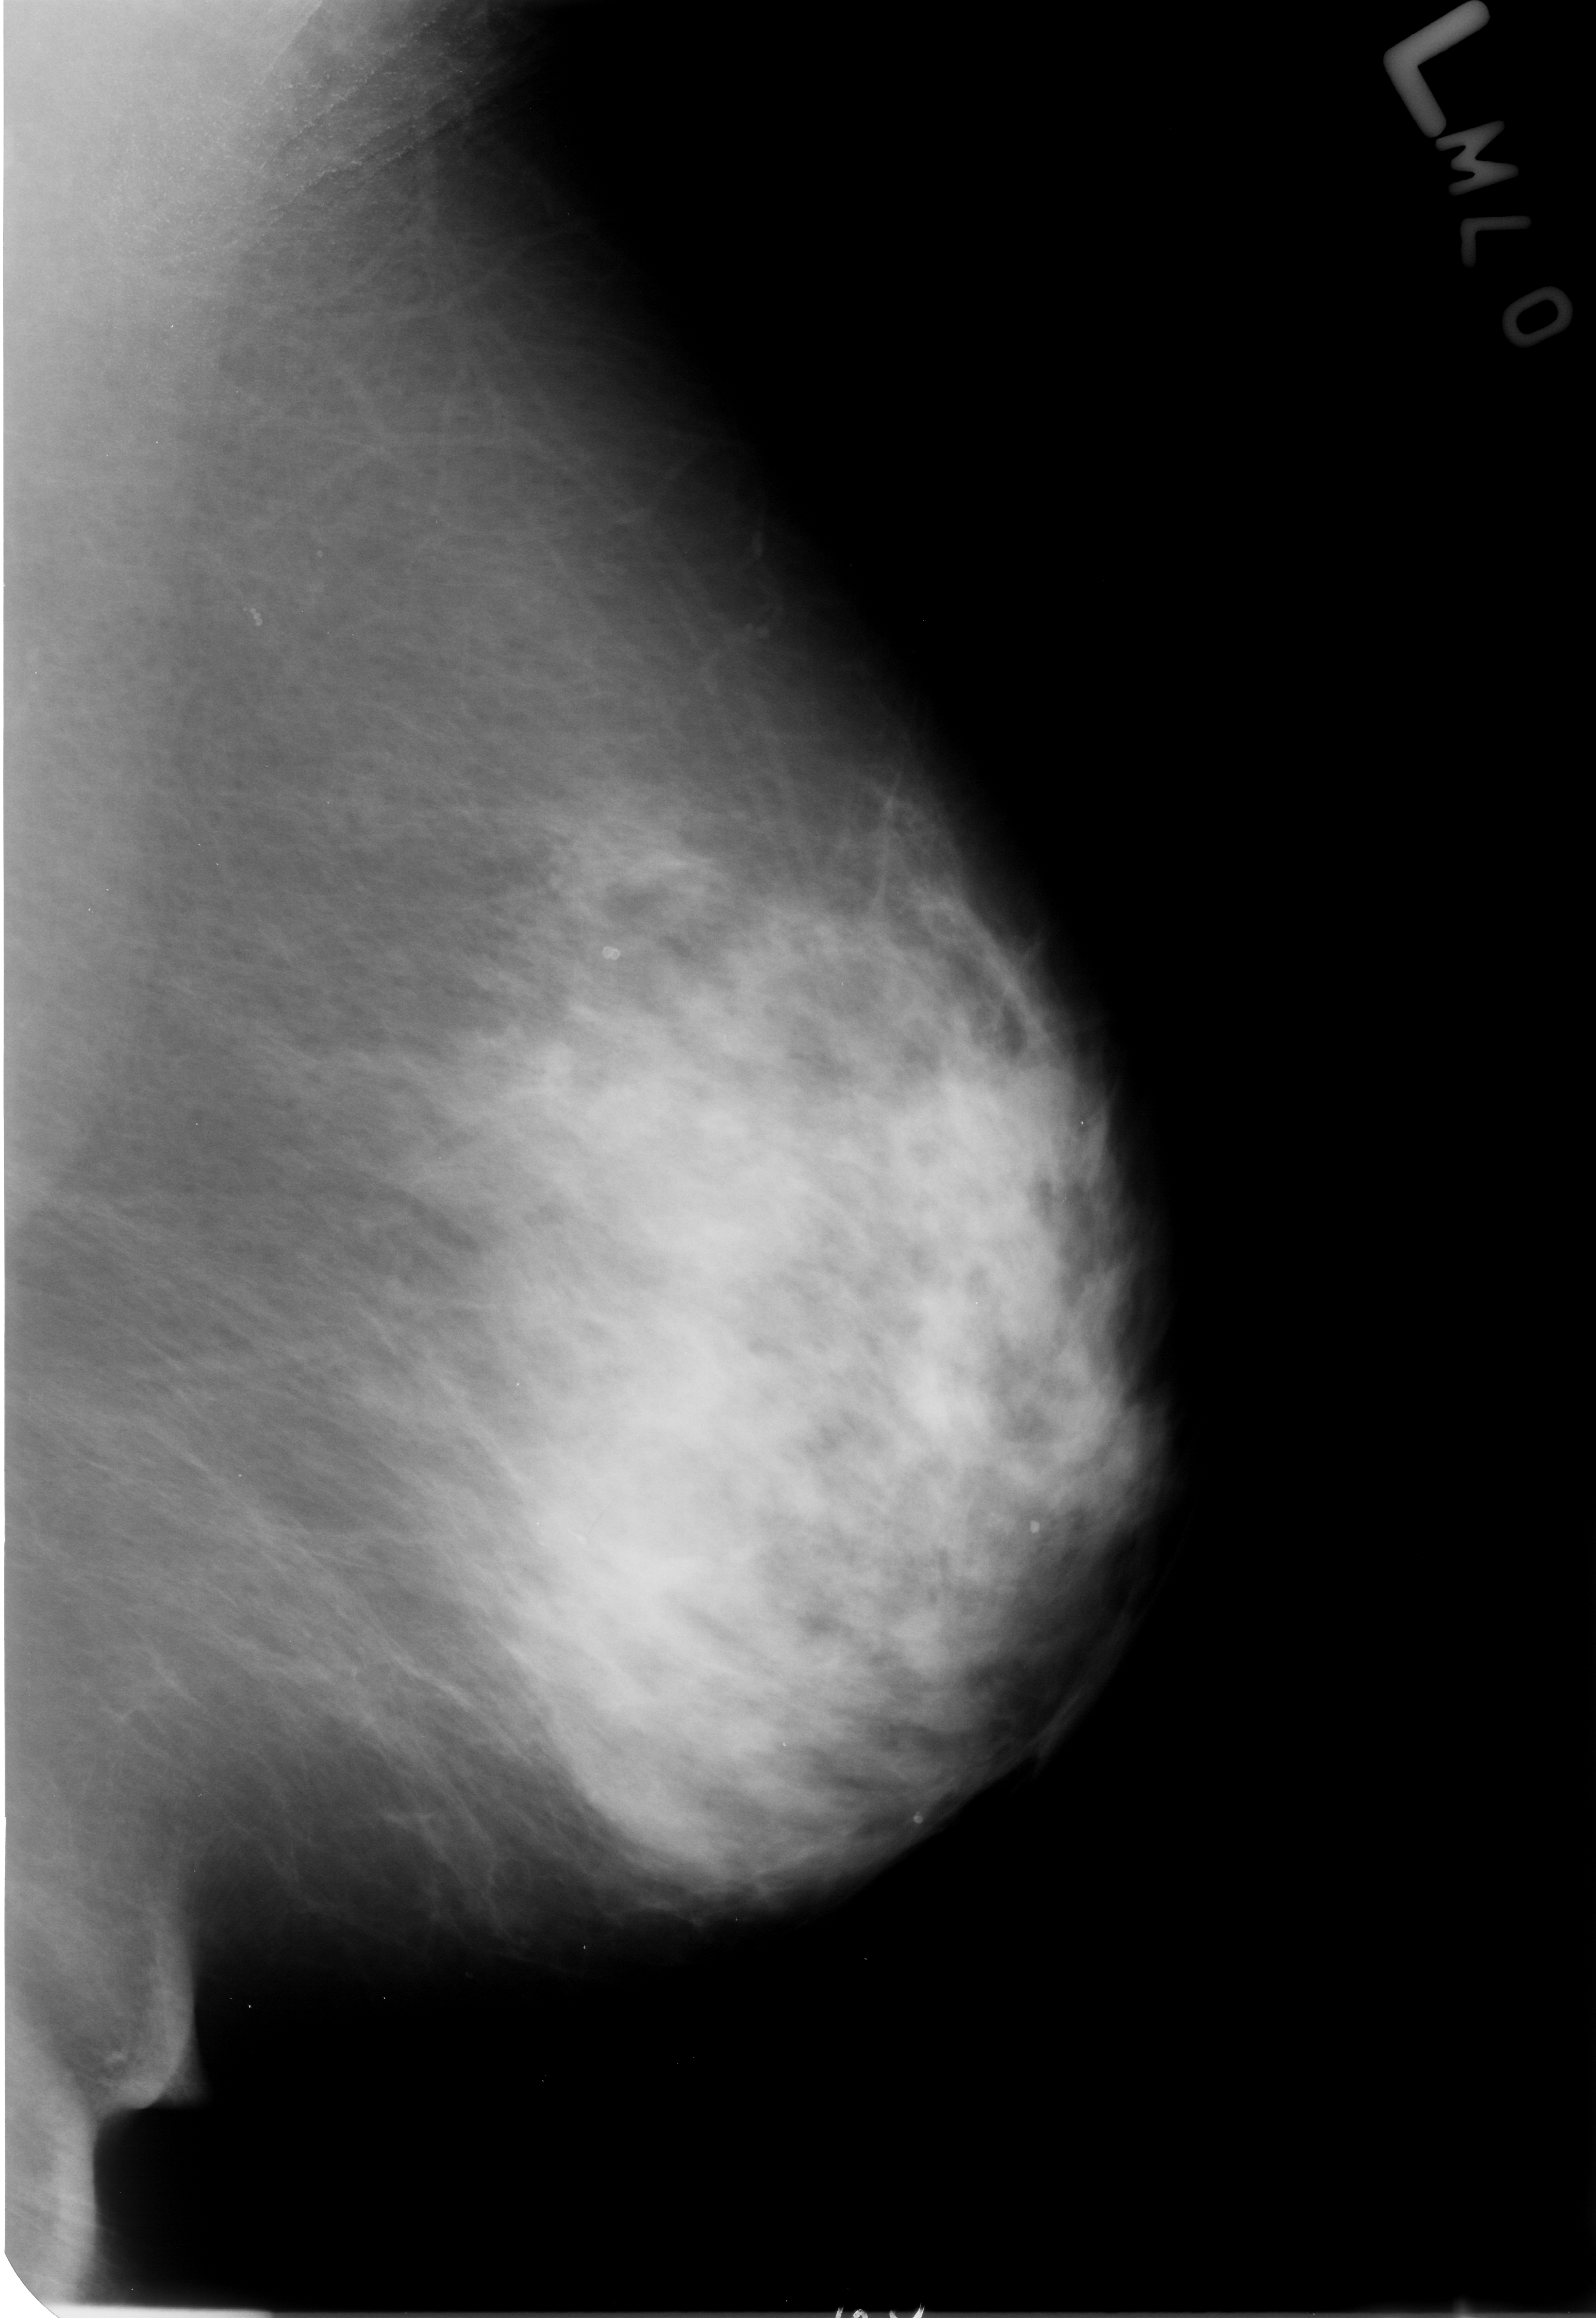
Scanned film-screen mammogram; left breast; MLO view; BI-RADS breast density category 3 (scale 1–4); 1596 × 2318 image matrix.
Expert-marked regions of interest on this film, with their recorded descriptors:
- Finding 1 of 4: calcifications, morphology round and regular / lucent centered; BI-RADS assessment category 2; subtlety rating 3 on a 1 (subtle) to 5 (obvious) scale; benign; no additional work-up was recommended (outcome (as recorded, no biopsy): benign without callback): bounding box [x1, y1, x2, y2] px = [552, 1517, 599, 1556]
- Finding 2 of 4: calcifications, morphology round and regular / lucent centered; BI-RADS assessment category 2; subtlety rating 3 on a 1 (subtle) to 5 (obvious) scale; benign; no additional work-up was recommended (outcome (as recorded, no biopsy): benign without callback): [589, 932, 632, 974]
- Finding 3 of 4: calcifications, morphology round and regular / lucent centered; BI-RADS assessment category 2; subtlety rating 3 on a 1 (subtle) to 5 (obvious) scale; outcome (as recorded, no biopsy): benign without callback (not worked up further): [903, 1790, 937, 1836]
- Finding 4 of 4: calcifications, morphology round and regular / lucent centered; BI-RADS assessment category 2; benign; no additional work-up was recommended (outcome (as recorded, no biopsy): benign without callback): [1010, 1501, 1057, 1552]